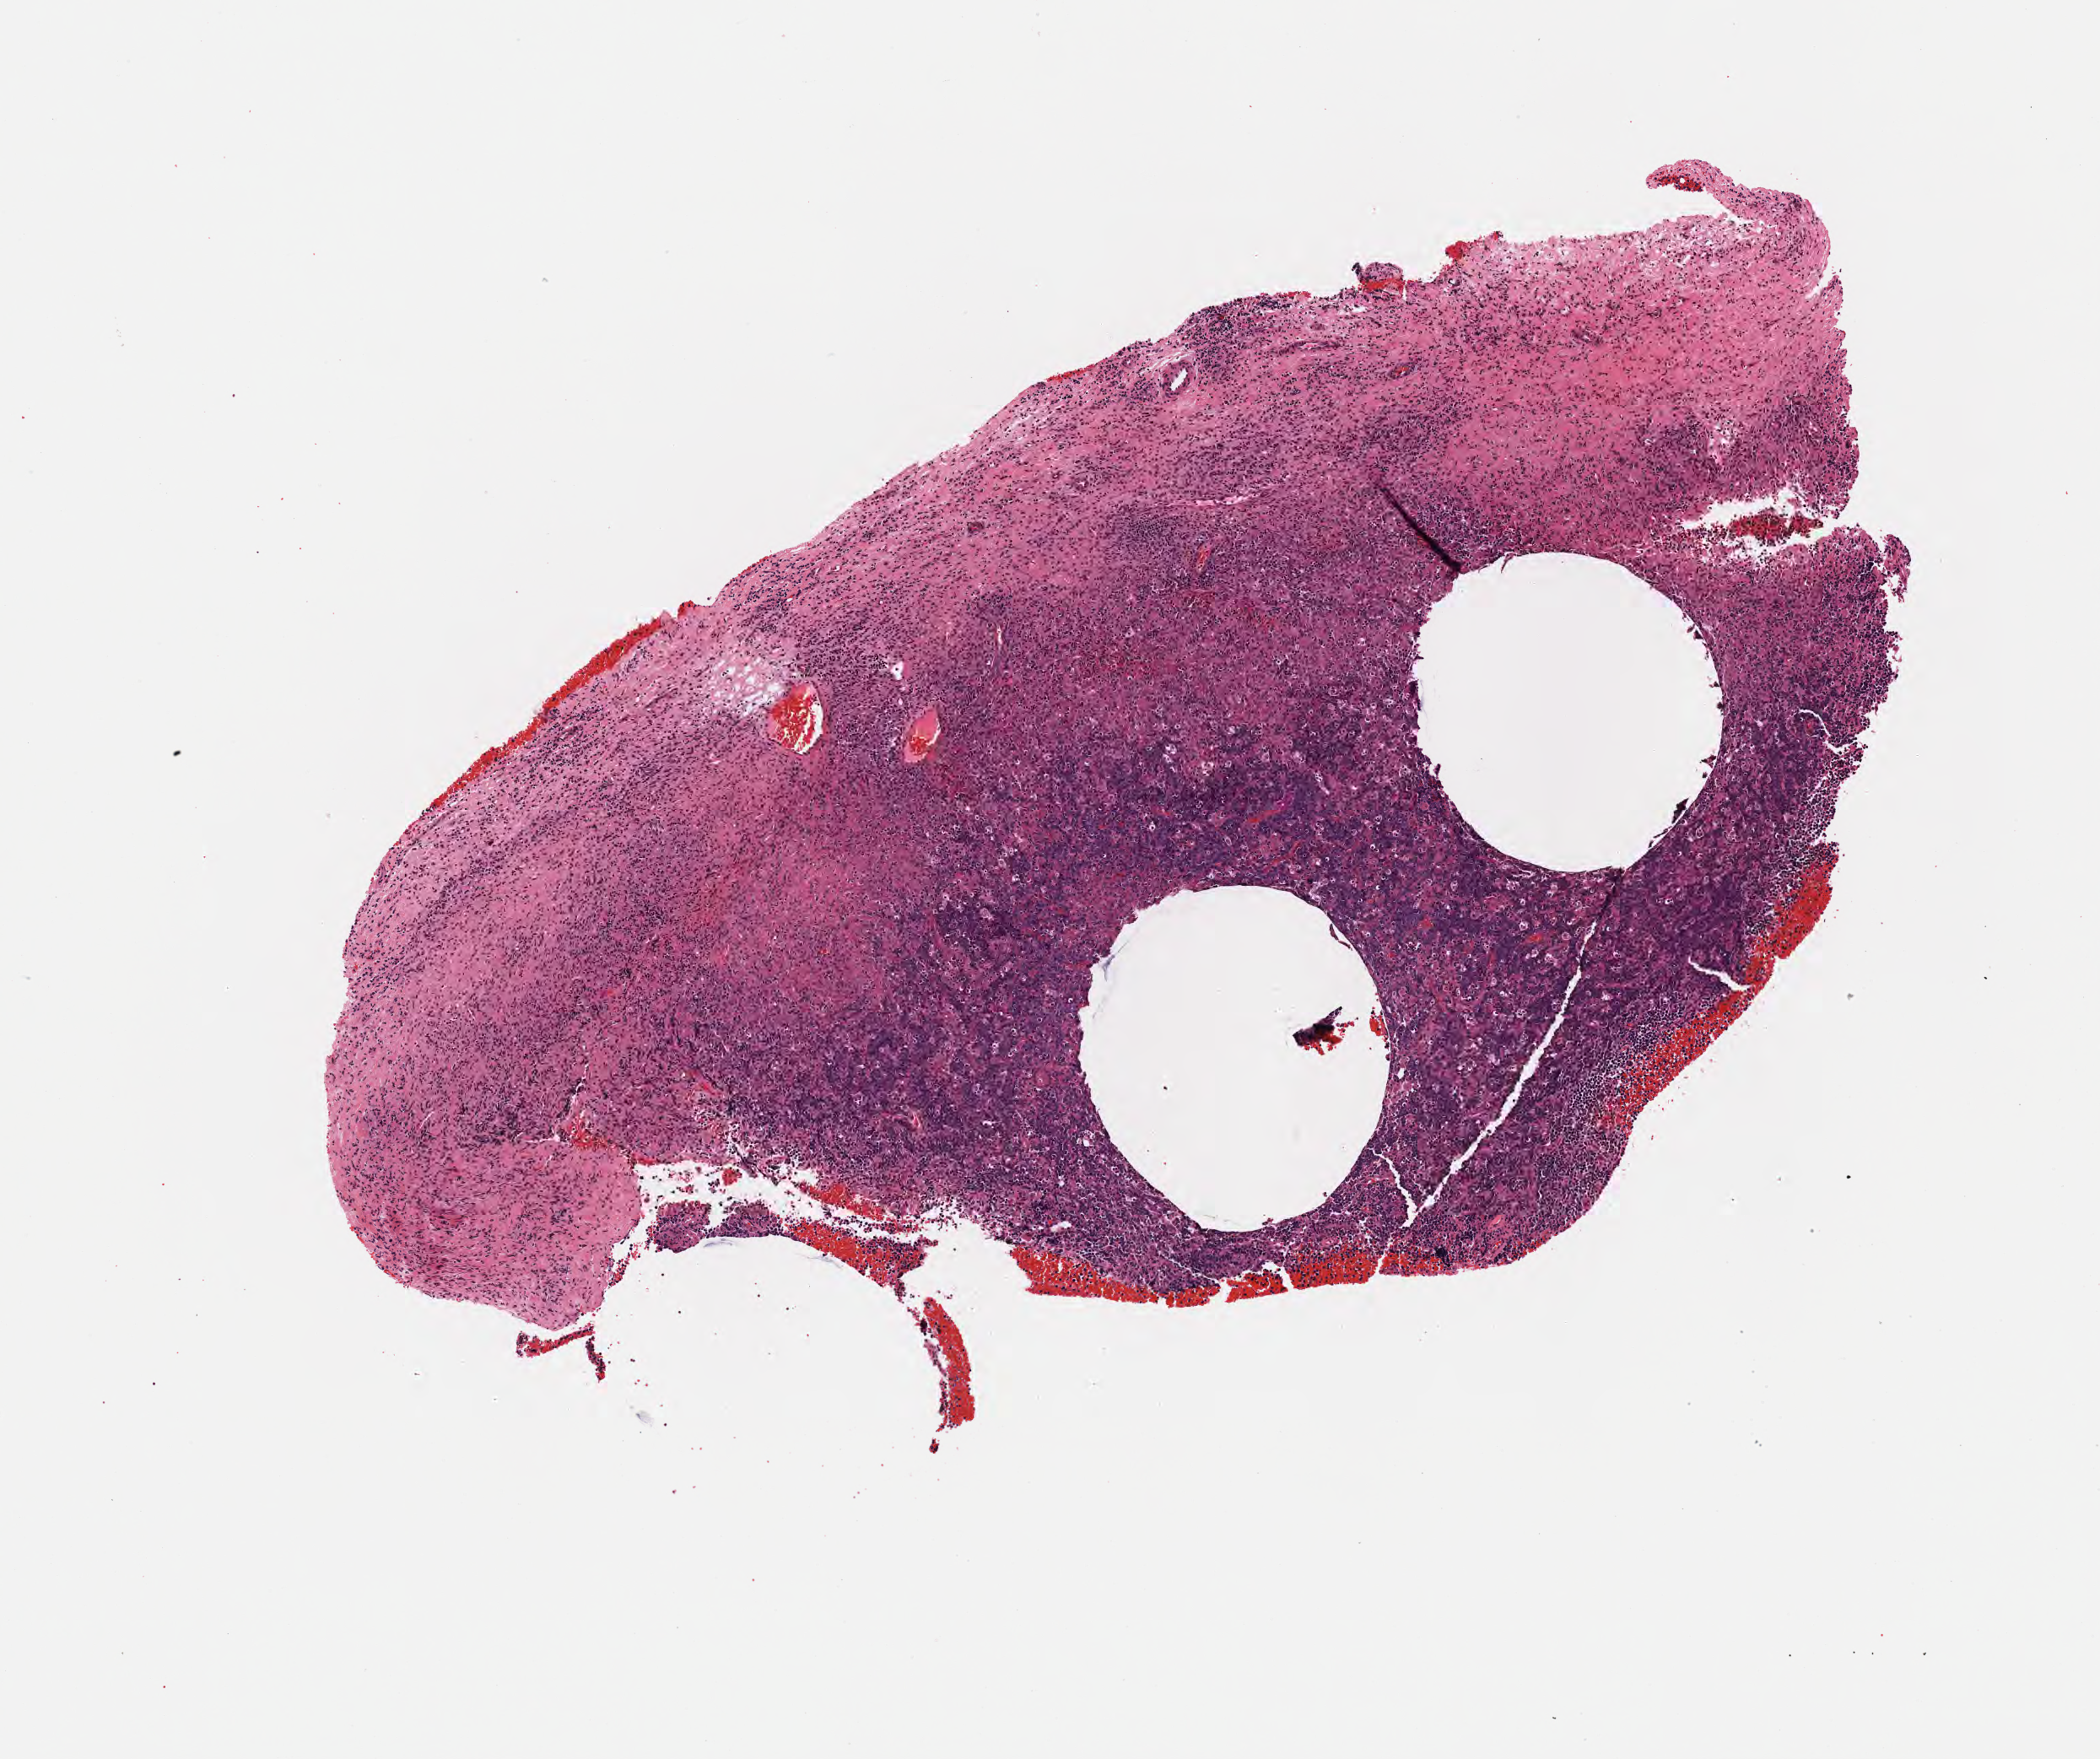
Whole-slide image, haematoxylin and eosin stain, a low-resolution overview of the entire scanned area, about 5.0 x 4.2 mm, formalin-fixed, paraffin-embedded (FFPE) tissue, specimen: primary tumor, anatomic site: lymph node of head and neck. Male, age 5 years at initial diagnosis. Slide review estimates, as recorded: tumor cells 60%, tumor nuclei 85%, stromal cells 10%, necrosis 20%, normal cells 10%. Infiltration values recorded for this section: lymphocyte infiltration 60%, monocyte infiltration 30%, neutrophil infiltration 10%.
Ann Arbor stage (patient): Stage I. Histologic diagnosis: Burkitt lymphoma, NOS. Section: bottom of the tissue portion.